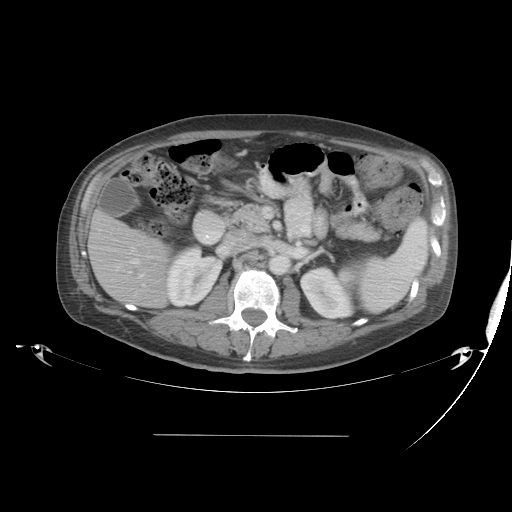
Contrast-enhanced abdominal CT, one axial slice. Position 19 of 48 along the scan axis. 120 kVp. Intravenous contrast given. Soft-tissue window (W 400 / L 40 HU). 512 × 512 image matrix, field of view 486 × 486 mm. Male patient, age 65 years. From the clinical record (not read from this slice): diagnosis: colorectal cancer liver metastases, imaged before liver resection; multiple liver metastases: yes; largest metastasis: 11 cm; disease in both lobes: yes.
Outlined on this slice (outlined manually by an expert reader):
- hepatic veins: bounding box [x1, y1, x2, y2] px = [130, 259, 139, 264]
- liver: [90, 213, 171, 308]
- portal vein (with intrahepatic branches): [98, 233, 145, 286]
- liver metastasis: [130, 267, 139, 277]